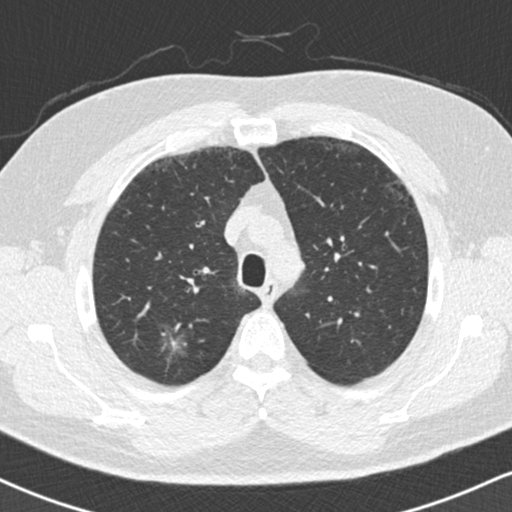
Chest CT (low-dose screening protocol), one axial image; second annual screen; lung window (W 1500 / L -600 HU); slice 42 of 169 in the series. Male participant, aged 59 years at enrolment.
Expert reader's lesion annotation, bounding box <152,309,205,363> (left, top, right, bottom; pixels). Reader record for this screening exam (exam-level; its link to the box is not recorded): non-calcified nodule or mass ≥4 mm, right upper lobe, 18 × 16 mm, ground glass attenuation, pre-existing on the prior screen: yes. Official screen result: positive, no significant change: stable abnormalities potentially related to lung cancer, unchanged since the prior screening exam. Later outcome: lung cancer diagnosed 60 days after this screen — bronchiolo-alveolar adenocarcinoma, NOS, right lower lobe, stage IA (AJCC 6th edition), 15 mm at pathology.